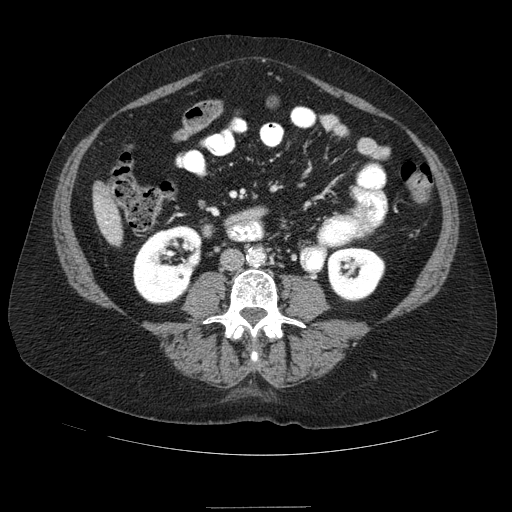
Contrast-enhanced abdominal CT (liver protocol), one axial slice; slice 12 of 89 in the series (ordered by position); reconstruction kernel STANDARD; 120 kVp; soft-tissue window (W 400 / L 40 HU); 512 × 512 image matrix. Case-level facts recorded for this patient, not image findings: diagnosis: hepatocellular carcinoma (patient treated with transarterial chemoembolisation; whether this scan precedes or follows treatment is not stated here); TNM stage (as recorded): Stage-IIIB; Child-Pugh class: A; tumour nodularity: multinodular.
Outlined on this slice (semi-automatically segmented with operator editing):
- liver parenchyma outside the tumour (the mass and vessels are separate outlines, so this box may not span the whole liver): bounding box <92,184,122,244> (left, top, right, bottom; pixels)